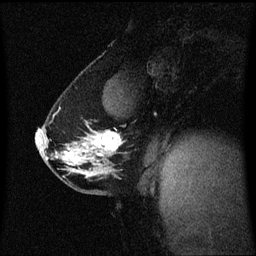
Breast MRI (dynamic contrast-enhanced), one sagittal slice; slice 38 of 60 in the series (ordered by position); dynamic contrast-enhanced series, image 2 of 3 at this slice position (ordered by acquisition); 1.5 T; TE 4.2 ms, TR 8.4 ms; 2 mm slice thickness; 256 × 256 image matrix, field of view 210 × 210 mm. Patient: female, 40 years. From the clinical record (not read from this slice): setting: breast cancer imaged before/during neoadjuvant chemotherapy; receptor status: triple-negative.
Outlined on this slice (semi-automatically segmented with operator editing):
- analysis volume of interest (the breast-tissue region the enhancement analysis was run in; not a lesion): bounding box [x1, y1, x2, y2] px = [36, 112, 126, 188]
- tumour enhancement mask (voxels above the 70 % enhancement threshold inside the analysis volume of interest): [36, 132, 122, 162]